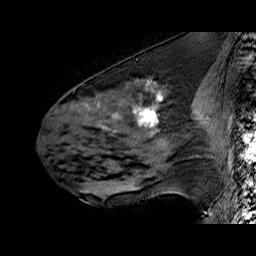
Breast MRI (dynamic contrast-enhanced), one sagittal slice; slice 27 of 60 in the series (ordered by position); dynamic contrast-enhanced series, time point 2 of 6 at this slice position (early post-contrast); 1.5 T; TE 6.4 ms, TR 32.9 ms; 4 mm slice thickness; 256 × 256 image matrix. Female patient. Case-level facts recorded for this patient, not image findings: setting: breast cancer imaged before/during neoadjuvant chemotherapy; receptor status: HER2-positive.
Outlined on this slice (semi-automatically segmented with operator editing):
- analysis volume of interest (the breast-tissue region the enhancement analysis was run in; not a lesion): bounding box <51,78,196,160> (left, top, right, bottom; pixels)
- tumour enhancement mask (voxels above the 100 % enhancement threshold inside the analysis volume of interest): <86,81,163,129>